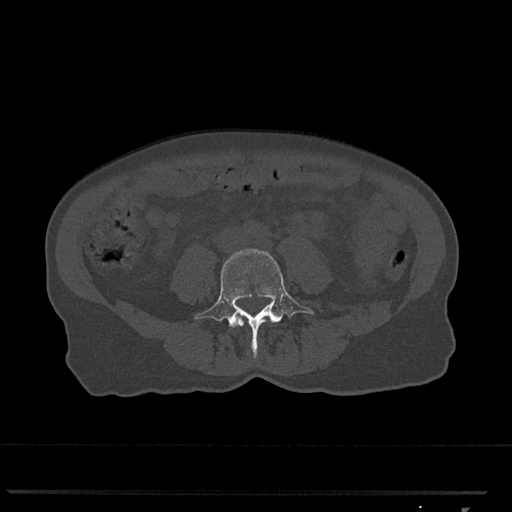
CT including the spine, one axial slice; slice 217 of 793 in the series (ordered by position); reconstruction kernel Br40s/3; bone window (W 1800 / L 400 HU); 512 × 512 image matrix, field of view 380 × 380 mm. Female patient, age 62 years. Case-level facts recorded for this patient, not image findings: primary cancer: renal.
Annotated regions visible in this slice (semi-automatic segmentation, software-assisted and operator-edited):
- L3 vertebra: box from (x=241, y=323) to (x=244, y=327) px
- L4 vertebra: (x=194, y=248)–(x=315, y=357)